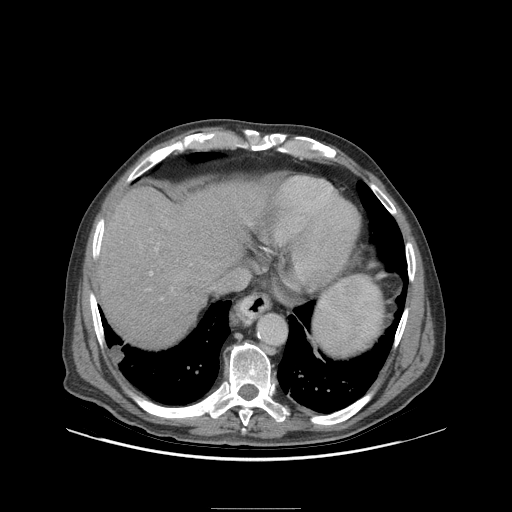
Contrast-enhanced abdominal CT (liver protocol), one axial slice. 140 kVp. Soft-tissue window (W 400 / L 40 HU). 2.5 mm slice thickness. 512 × 512 image matrix. From the clinical record (not read from this slice): diagnosis: hepatocellular carcinoma (patient treated with transarterial chemoembolisation; whether this scan precedes or follows treatment is not stated here); TNM stage (as recorded): Stage-I; Child-Pugh class: A.
Structures marked on this image (semi-automatically segmented with operator editing):
- abdominal aorta: bounding box (x1, y1, x2, y2) in pixels: (260, 315, 285, 343)
- liver parenchyma outside the tumour (the mass and vessels are separate outlines, so this box may not span the whole liver): (96, 182, 272, 344)
- liver vessels: (150, 272, 153, 275)